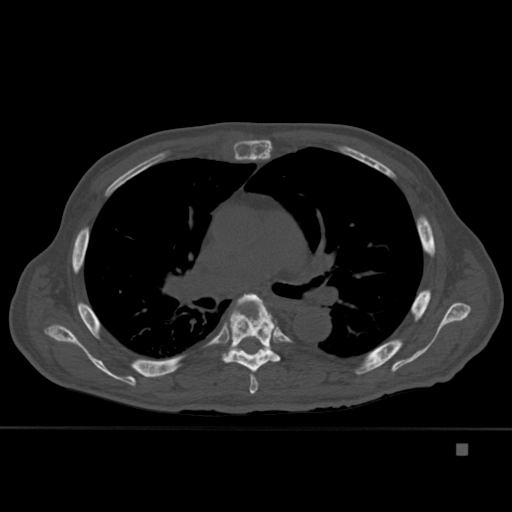
CT including the spine, one axial slice; slice 295 of 451 in the series (ordered by position); bone window (W 1800 / L 400 HU); 1.5 mm slice thickness; 512 × 512 image matrix, field of view 378 × 378 mm. Patient: male, 75 years. From the clinical record (not read from this slice): primary cancer: prostate.
Structures marked on this image (semi-automatic segmentation, software-assisted and operator-edited):
- T5 vertebra: bounding box [x1, y1, x2, y2] px = [232, 293, 265, 394]
- T6 vertebra: [221, 300, 281, 372]
- T7 vertebra: [237, 348, 249, 354]